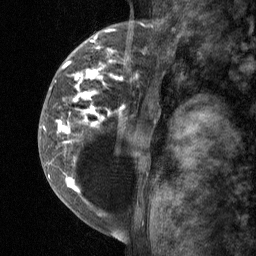
Breast MRI (dynamic contrast-enhanced), one sagittal slice. Dynamic contrast-enhanced study with each time point stored as its own series, time point 2 of 3 at this slice position (early post-contrast, ordered by acquisition time). 1.5 T. TE 4.8 ms, TR 27 ms. 2 mm slice thickness. 256 × 256 image matrix. Female patient, age 34 years. Case-level facts recorded for this patient, not image findings: setting: breast cancer imaged before/during neoadjuvant chemotherapy; receptor status: HR-positive, HER2-negative.
Outlined on this slice (semi-automatic segmentation, software-assisted and operator-edited):
- analysis volume of interest (the breast-tissue region the enhancement analysis was run in; not a lesion): bounding box <41,23,157,197> (left, top, right, bottom; pixels)
- tumour enhancement mask (voxels above the 90 % enhancement threshold inside the analysis volume of interest): <43,31,138,193>